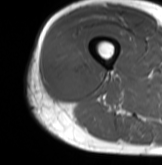
MRI of an extremity soft-tissue mass, one axial slice; position 28 of 61 along the scan axis; MR volume resampled by the dataset authors to the PET/CT grid (not the native acquisition matrix); 3.27 mm slice thickness; 162 × 165 image matrix, field of view 158 × 161 mm. Male patient. From the clinical record (not read from this slice): histological type: poorly differentiated synovial sarcoma; grade: high; site of the primary tumour: right buttock.
Annotated regions visible in this slice (expert contour drawn on MRI and transferred to this co-registered scan by the dataset authors):
- gross tumour volume including surrounding oedema: bounding box <48,31,92,98> (left, top, right, bottom; pixels)
- gross tumour volume (mass): <50,42,92,98>